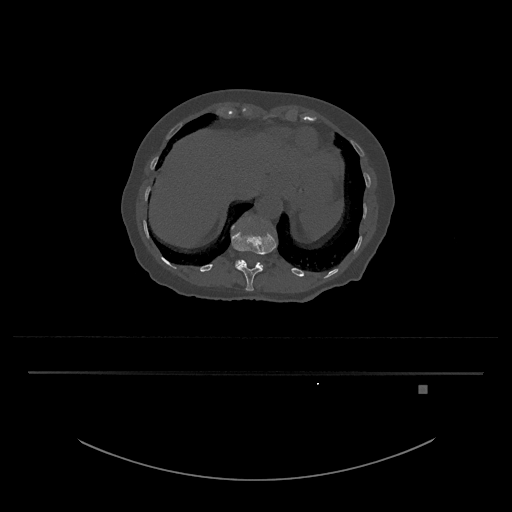
CT including the spine, one axial slice. Position 597 of 797 along the scan axis. Reconstruction kernel Br40s/3. 120 kVp. Bone window (W 1800 / L 400 HU). 512 × 512 image matrix, field of view 500 × 500 mm. Patient: female, 57 years. Case-level facts recorded for this patient, not image findings: primary cancer: cervical.
Structures marked on this image (semi-automatically segmented with operator editing):
- L1 vertebra: box from (x=235, y=260) to (x=264, y=268) px
- T12 vertebra: (x=231, y=225)–(x=276, y=291)